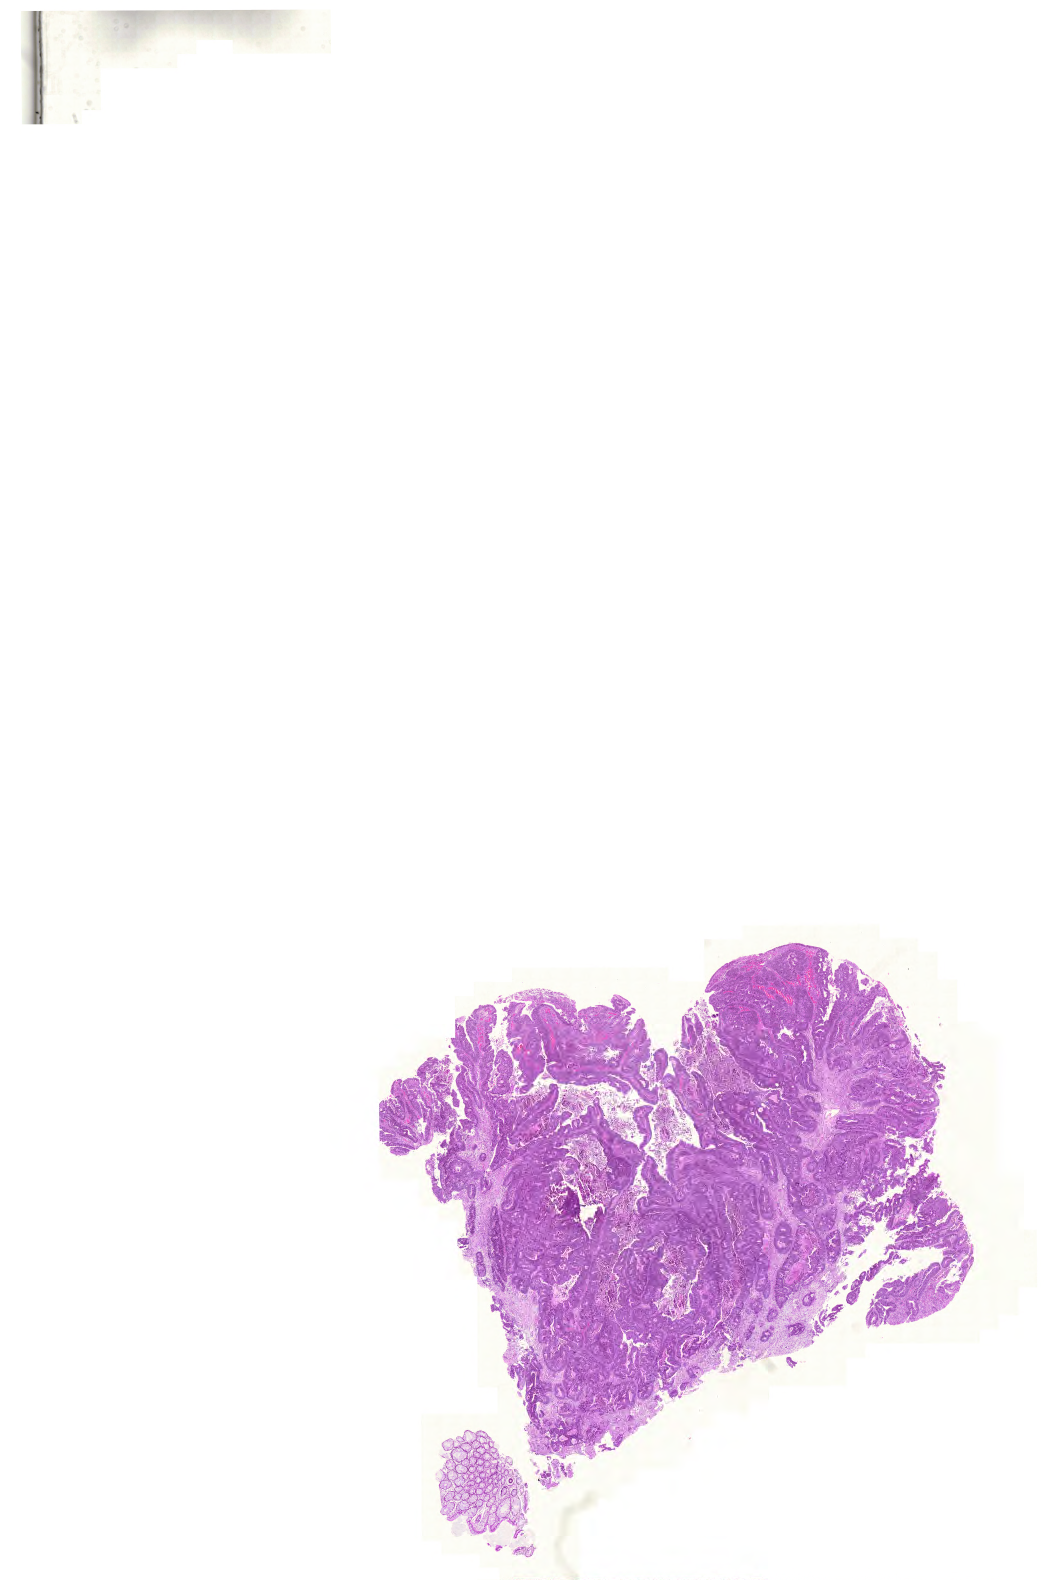
Digitized H&E-stained tissue section (whole slide), whole scanned area (about 15.5 x 23.5 mm, from a 20x scan) shown as a low-resolution overview. Formalin-fixed paraffin-embedded (FFPE) diagnostic section. Sample: primary tumour, colon. Male patient; age at initial diagnosis 80 years.
Diagnosis: Adenocarcinoma, NOS. Lymph nodes positive (case pathology): 2 of 13 examined. AJCC pathologic stage: IV (6th edition).